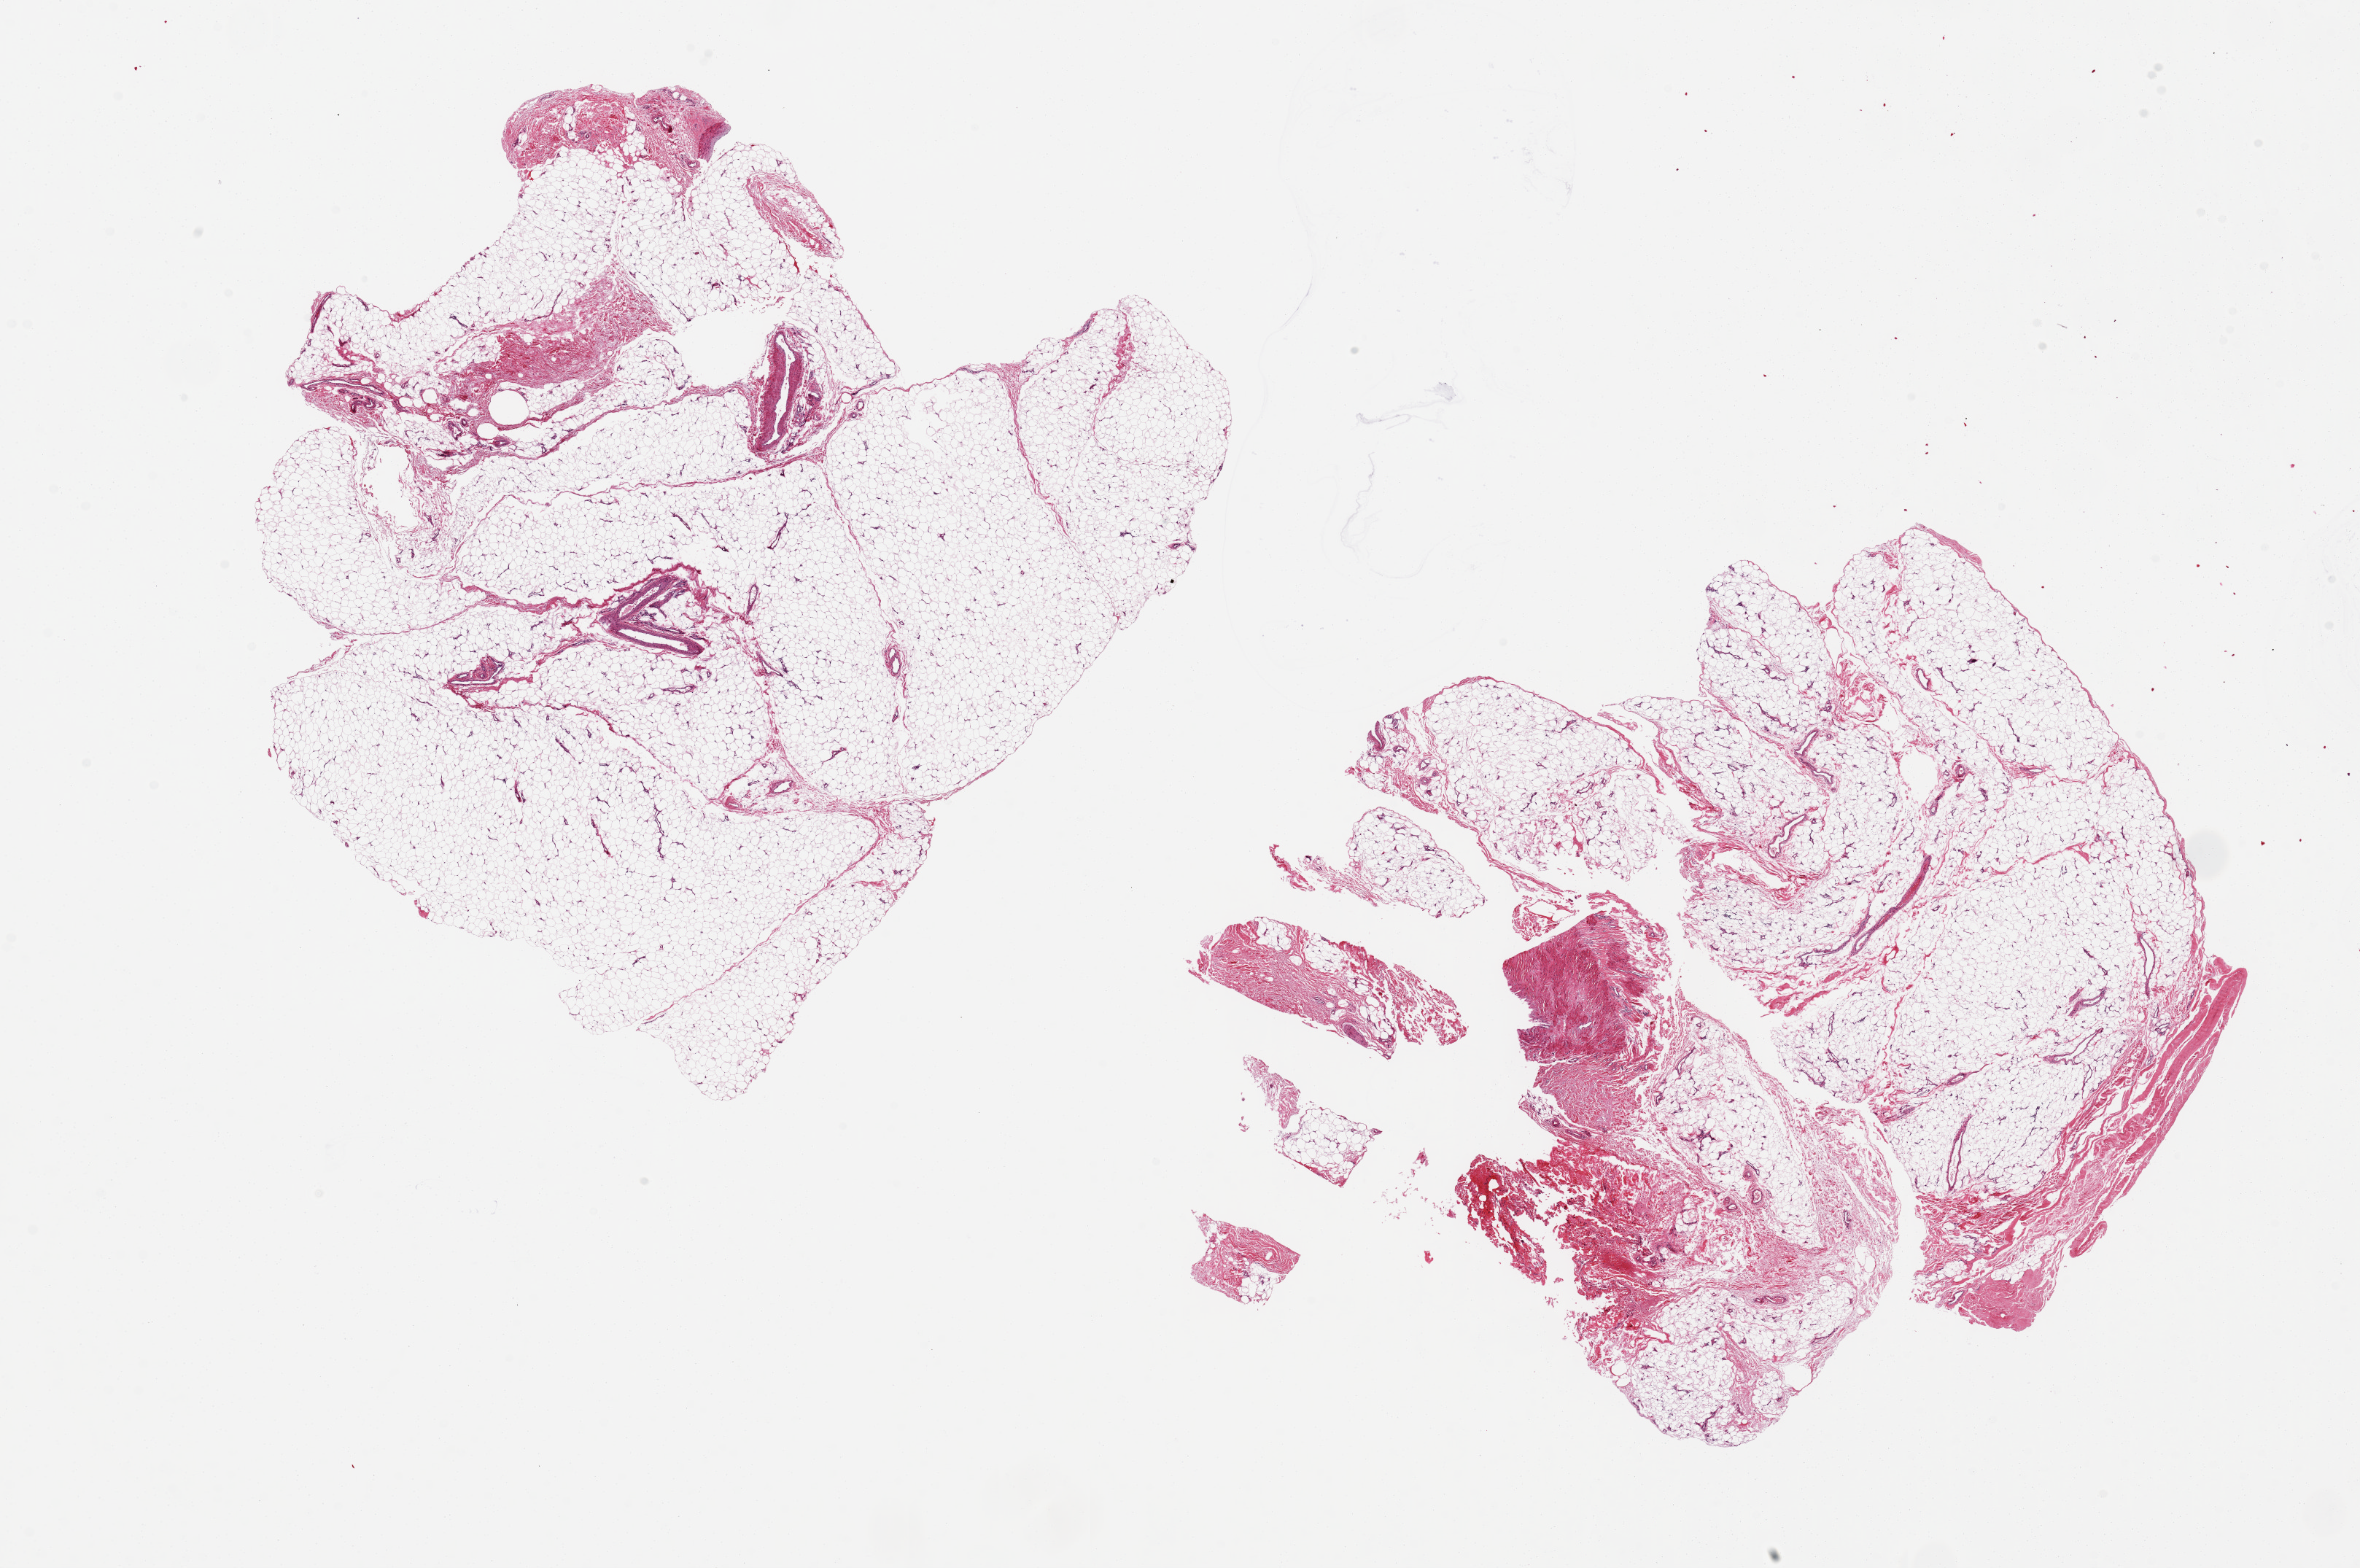
Whole-slide image, hematoxylin and eosin (H&E) stain, brightfield, low-resolution overview of the scanned area, about 25.6 x 17.0 mm, PAXgene-fixed paraffin-embedded (PFPE) section, section of adipose tissue (target tissue), donor tissue sample.
Pathologist's review note for this sample: 2 aliquots, ~13x10mm.